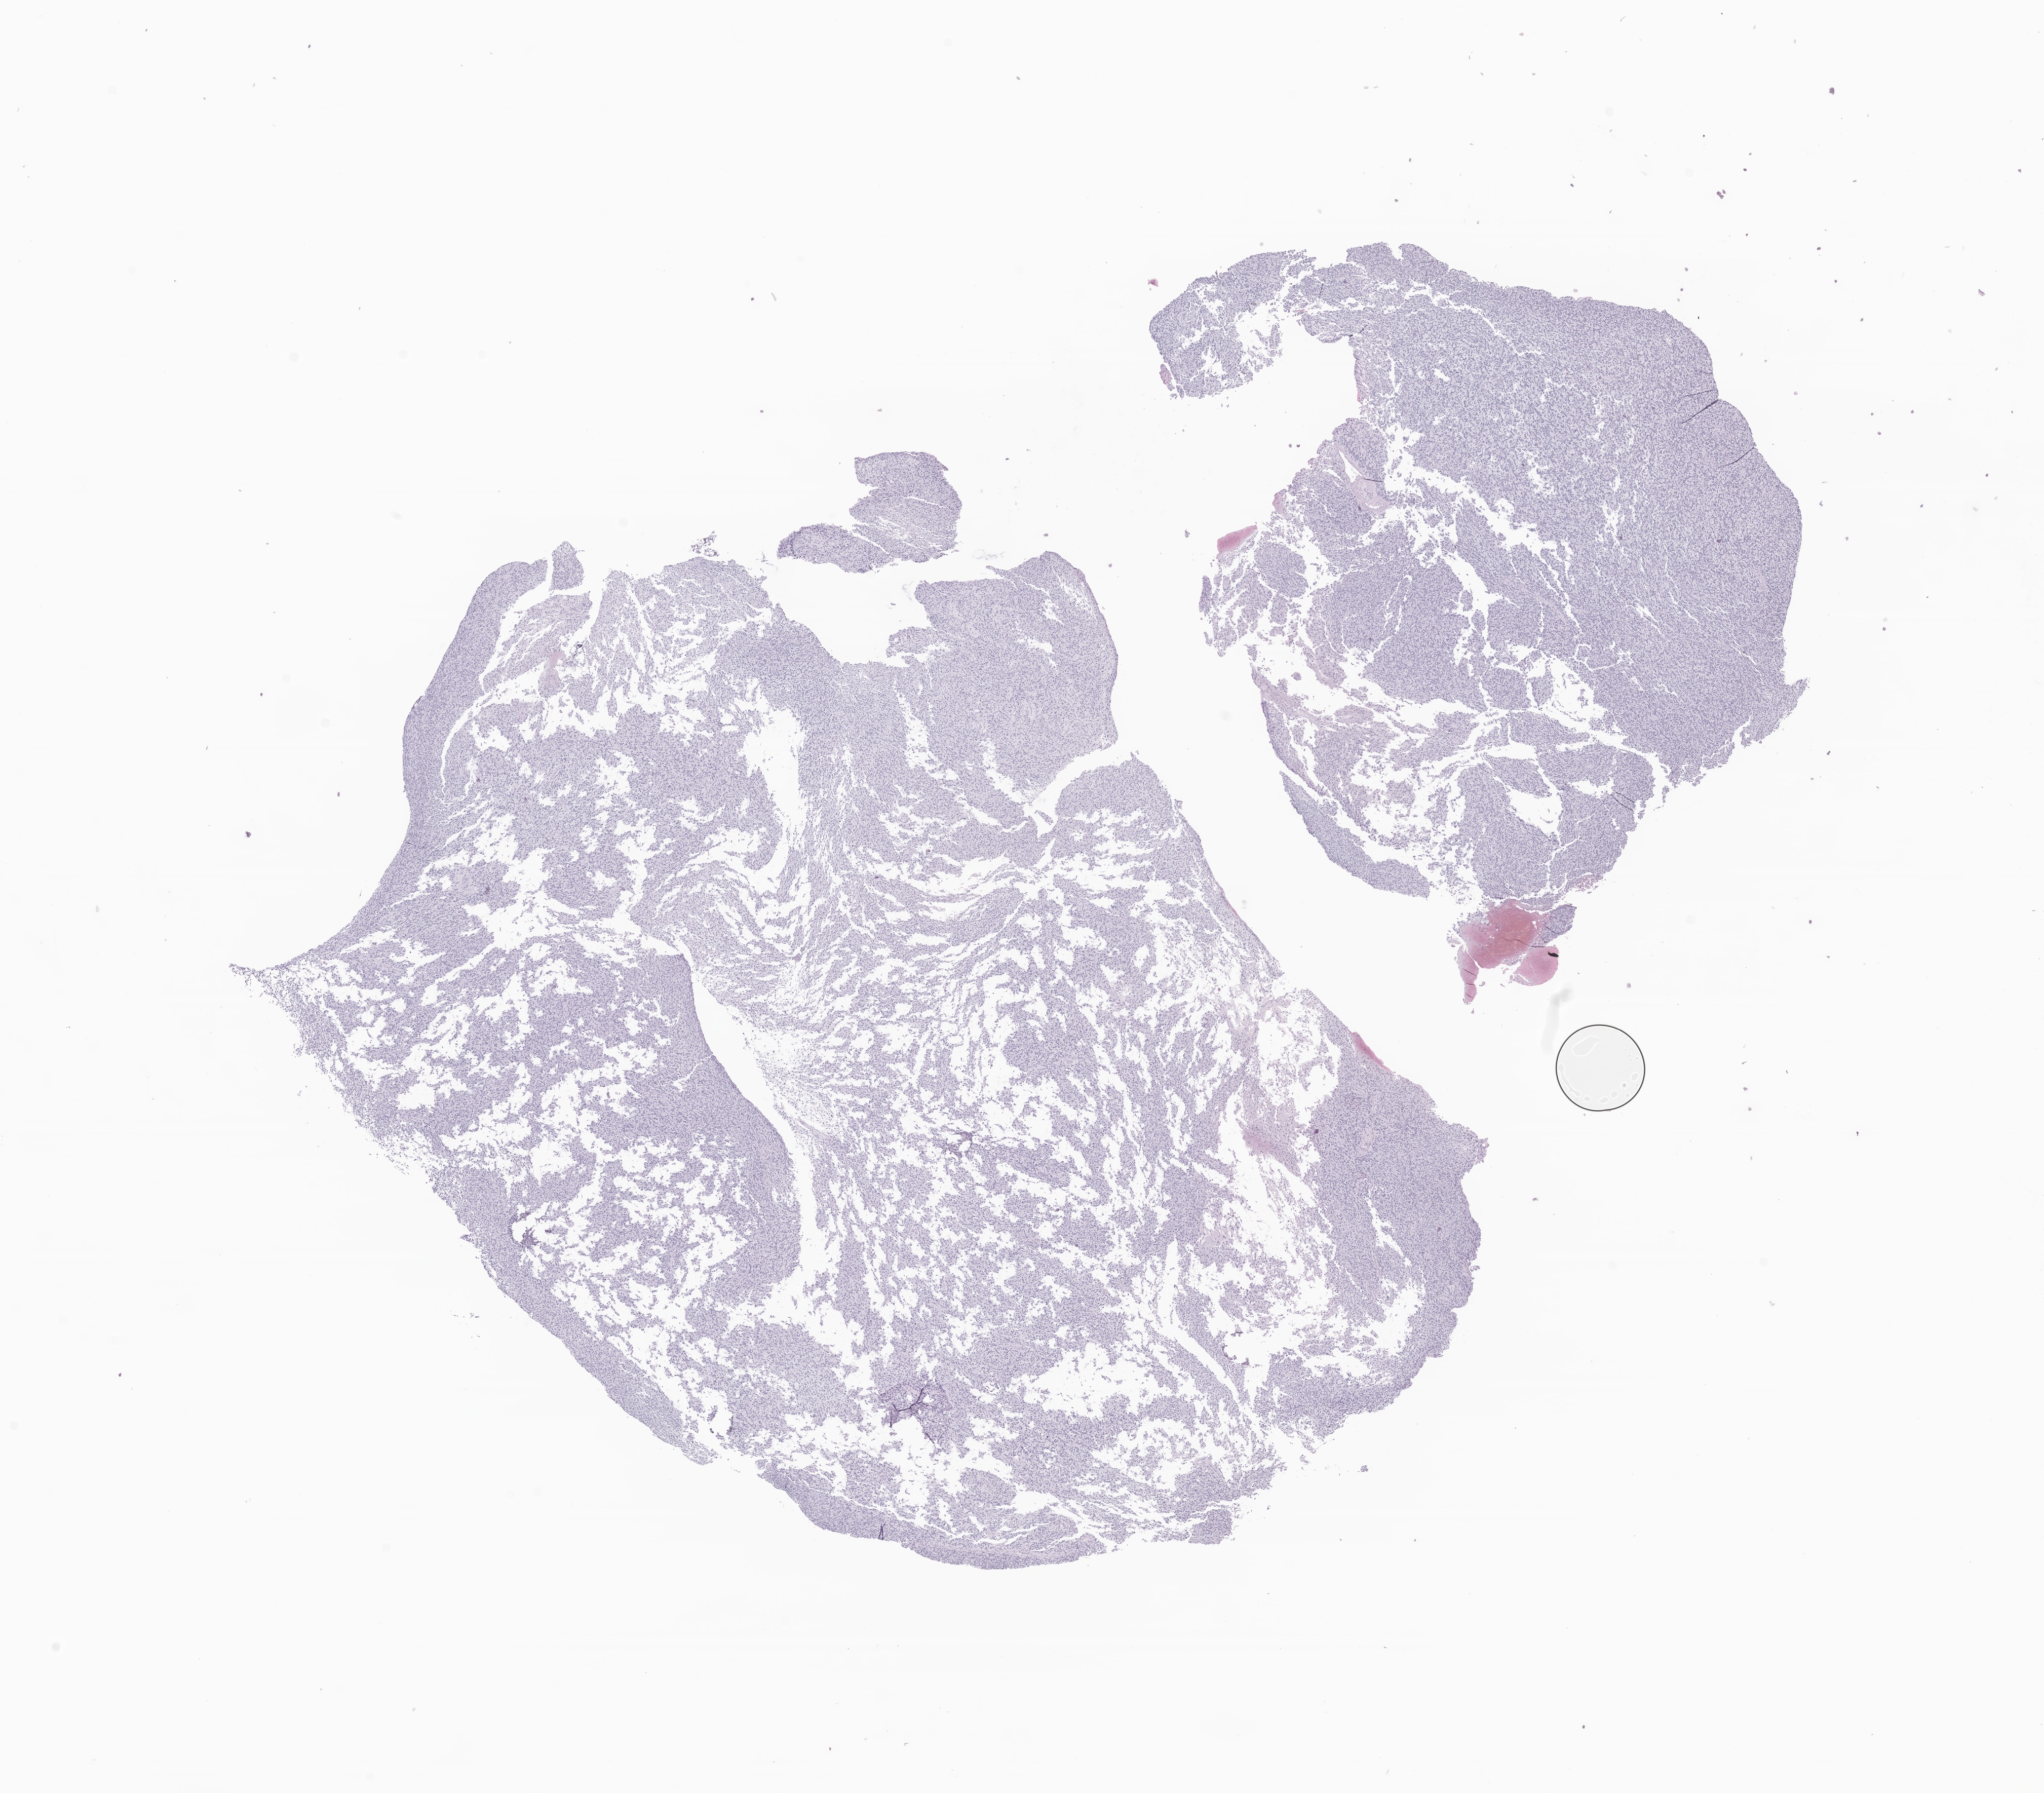
Digitized H&E-stained section of tumor tissue from the brain, low-resolution overview of the scanned area, about 17.0 x 14.9 mm. FFPE section. Female patient, age 183 months (15 years 3 months).
Diagnosis: Glioma, malignant.